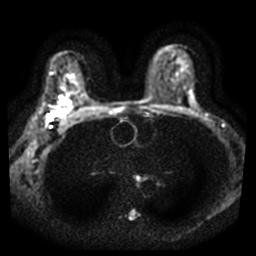
Breast MRI, one axial slice. Position 22 of 37 along the scan axis. Diffusion-weighted series; image 2 of 4 stored at this slice position (different b-values; order by instance number). 3 T. 5 mm slice thickness. 256 × 256 image matrix, field of view 340 × 340 mm. Female patient.
Structures marked on this image (manually delineated by an expert):
- tumour on diffusion-weighted imaging: bounding box (x1, y1, x2, y2) in pixels: (48, 112, 60, 121)